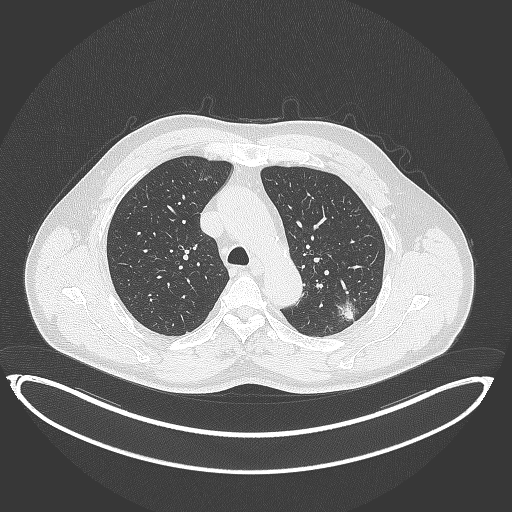
Chest CT, one axial slice. Reconstruction kernel B70f. Lung window (W 1500 / L -600 HU). 1 mm slice thickness. 512 × 512 image matrix, field of view 469 × 469 mm. Patient: male, 58 years. Case-level facts recorded for this patient, not image findings: clinical TNM (as recorded): T1c N0 M0; histopathological grade: G1-2.
Structures marked on this image (rectangle marked by the reading radiologist):
- lung tumour (recorded histology: adenocarcinoma): bounding box <334,296,362,330> (left, top, right, bottom; pixels)